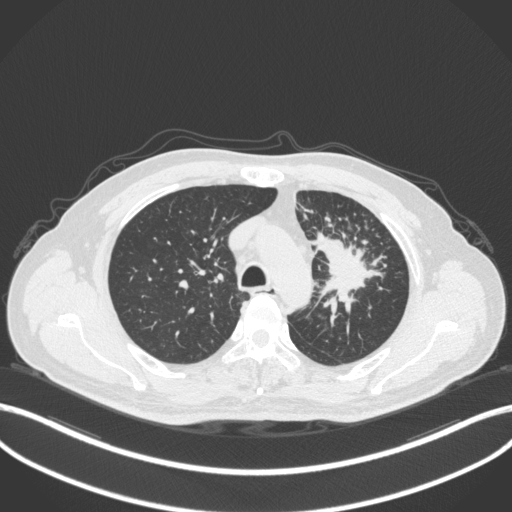
Chest CT, one axial slice; position 265 of 386 along the scan axis; reconstruction kernel B31f; 120 kVp; lung window (W 1500 / L -600 HU); 1 mm slice thickness; 512 × 512 image matrix, field of view 400 × 400 mm. Patient: male, 69 years. From the clinical record (not read from this slice): clinical TNM (as recorded): T2a N2 M0; histopathological grade: G2-3.
Structures marked on this image (rectangle marked by the reading radiologist):
- lung tumour (recorded histology: adenocarcinoma): bounding box [x1, y1, x2, y2] px = [314, 227, 393, 316]